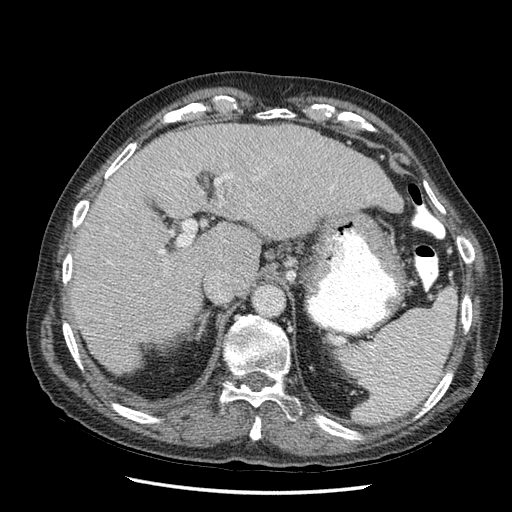
Contrast-enhanced abdominal CT (liver protocol), one axial slice. Slice 36 of 67 in the series (ordered by position). Soft-tissue window (W 400 / L 40 HU). 2.5 mm slice thickness. 512 × 512 image matrix, field of view 360 × 360 mm. From the clinical record (not read from this slice): diagnosis: hepatocellular carcinoma (patient treated with transarterial chemoembolisation; whether this scan precedes or follows treatment is not stated here); TNM stage (as recorded): Stage-I.
Annotated regions visible in this slice (semi-automatic segmentation, software-assisted and operator-edited):
- liver parenchyma outside the tumour (the mass and vessels are separate outlines, so this box may not span the whole liver): bounding box [x1, y1, x2, y2] px = [70, 122, 402, 376]
- liver vessels: [153, 171, 248, 281]